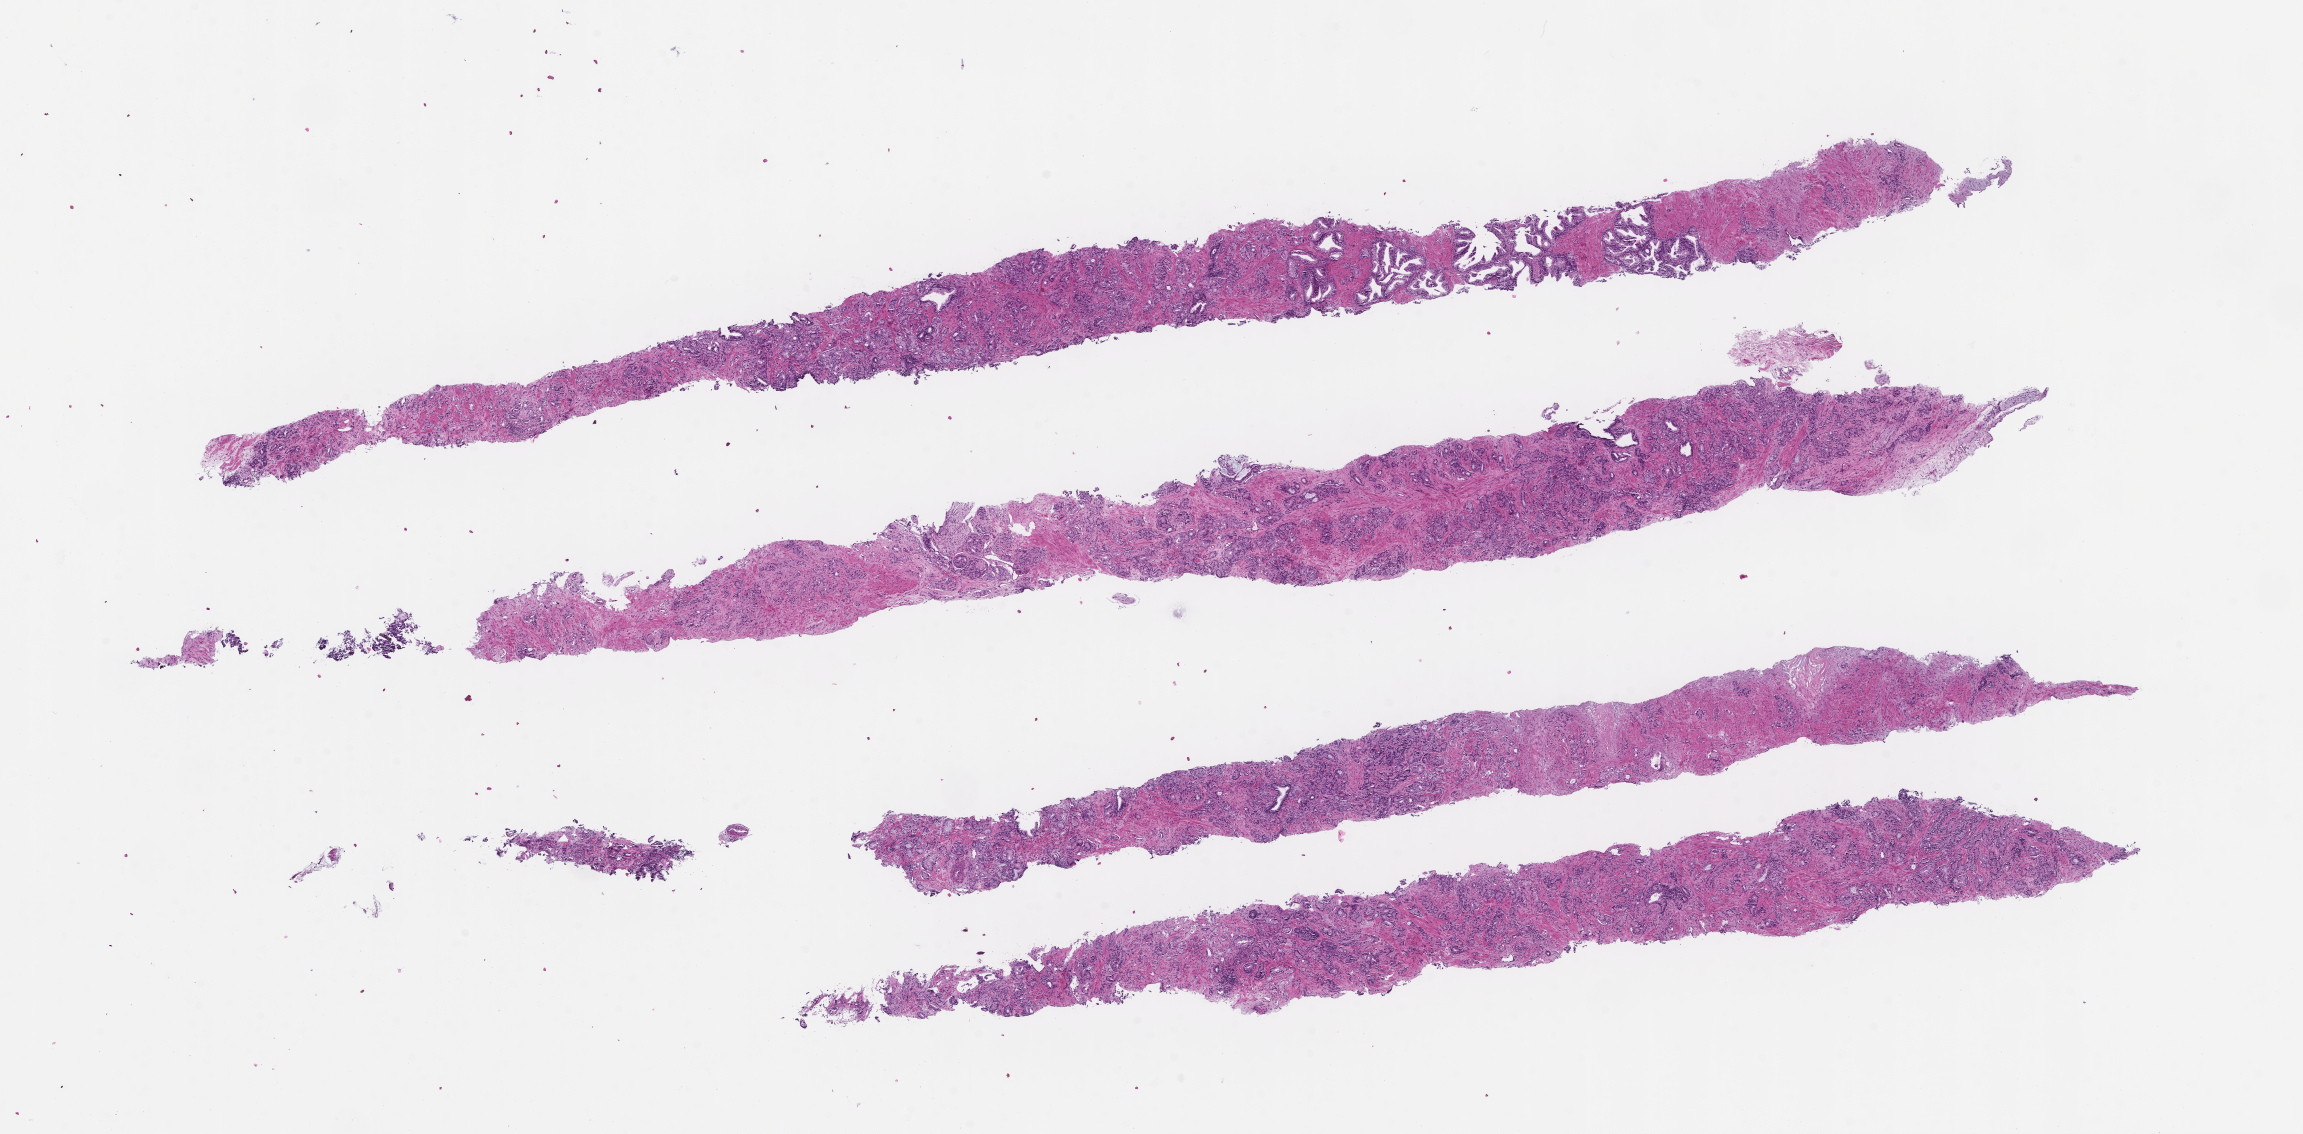
Digitized hematoxylin and eosin (H&E)-stained section — a low-resolution overview of the entire scanned area, about 18.6 x 9.2 mm. Formalin-fixed paraffin-embedded section. Site: prostate. Specimen time point: archival tissue. Patient sex: male.
- this section: primary tumour tissue
- diagnosis: Prostate Carcinoma